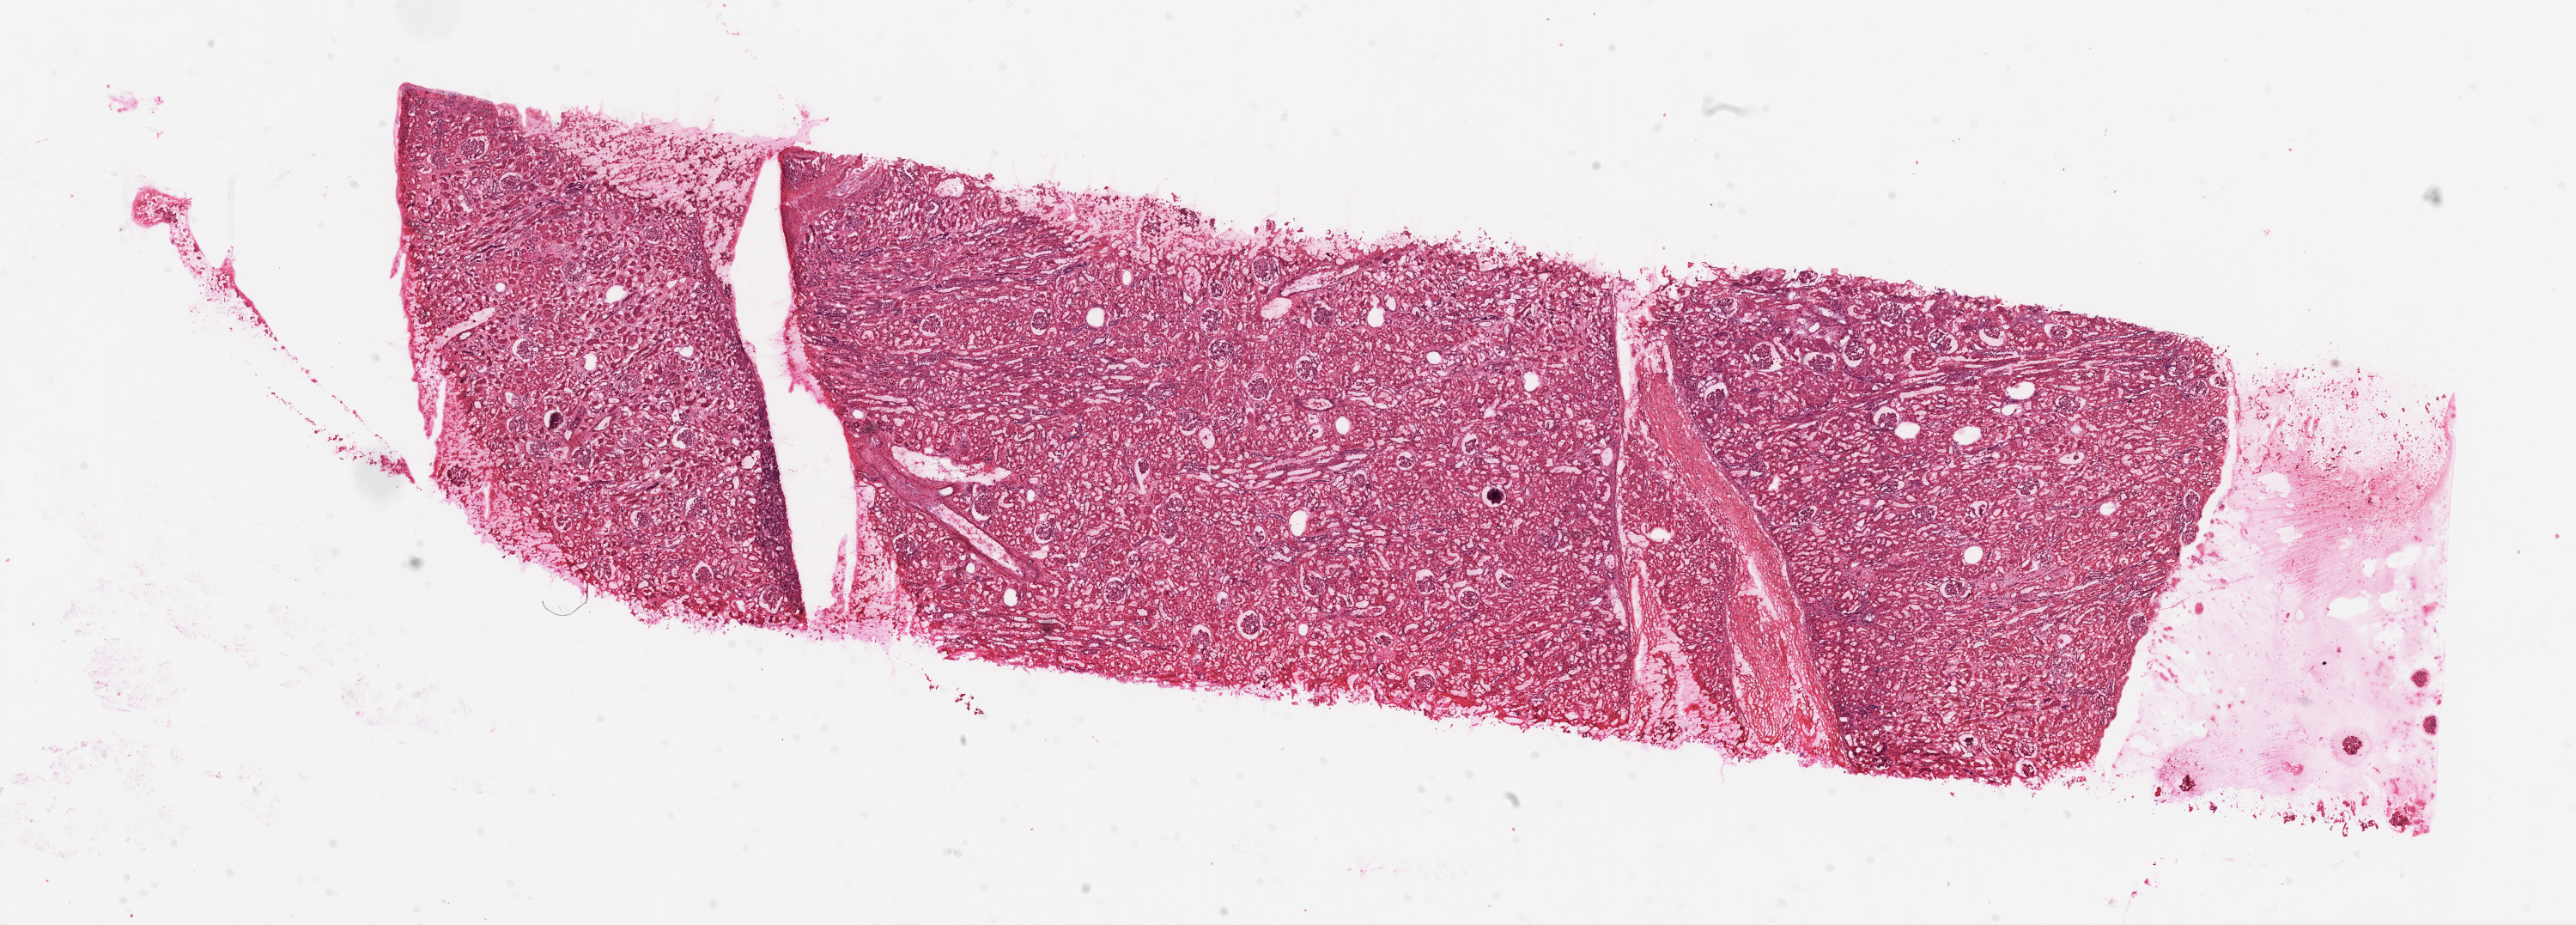
Whole-slide histology image, H&E, shown as a low-resolution overview of the whole scanned area (about 24.1 x 8.6 mm); frozen section; solid tissue normal (non-tumour tissue) sample from the kidney. Patient: male, age at initial diagnosis 49 years.
This section: solid tissue normal (non-tumour) sample from the same patient. Patient diagnosis: Clear cell adenocarcinoma, NOS.